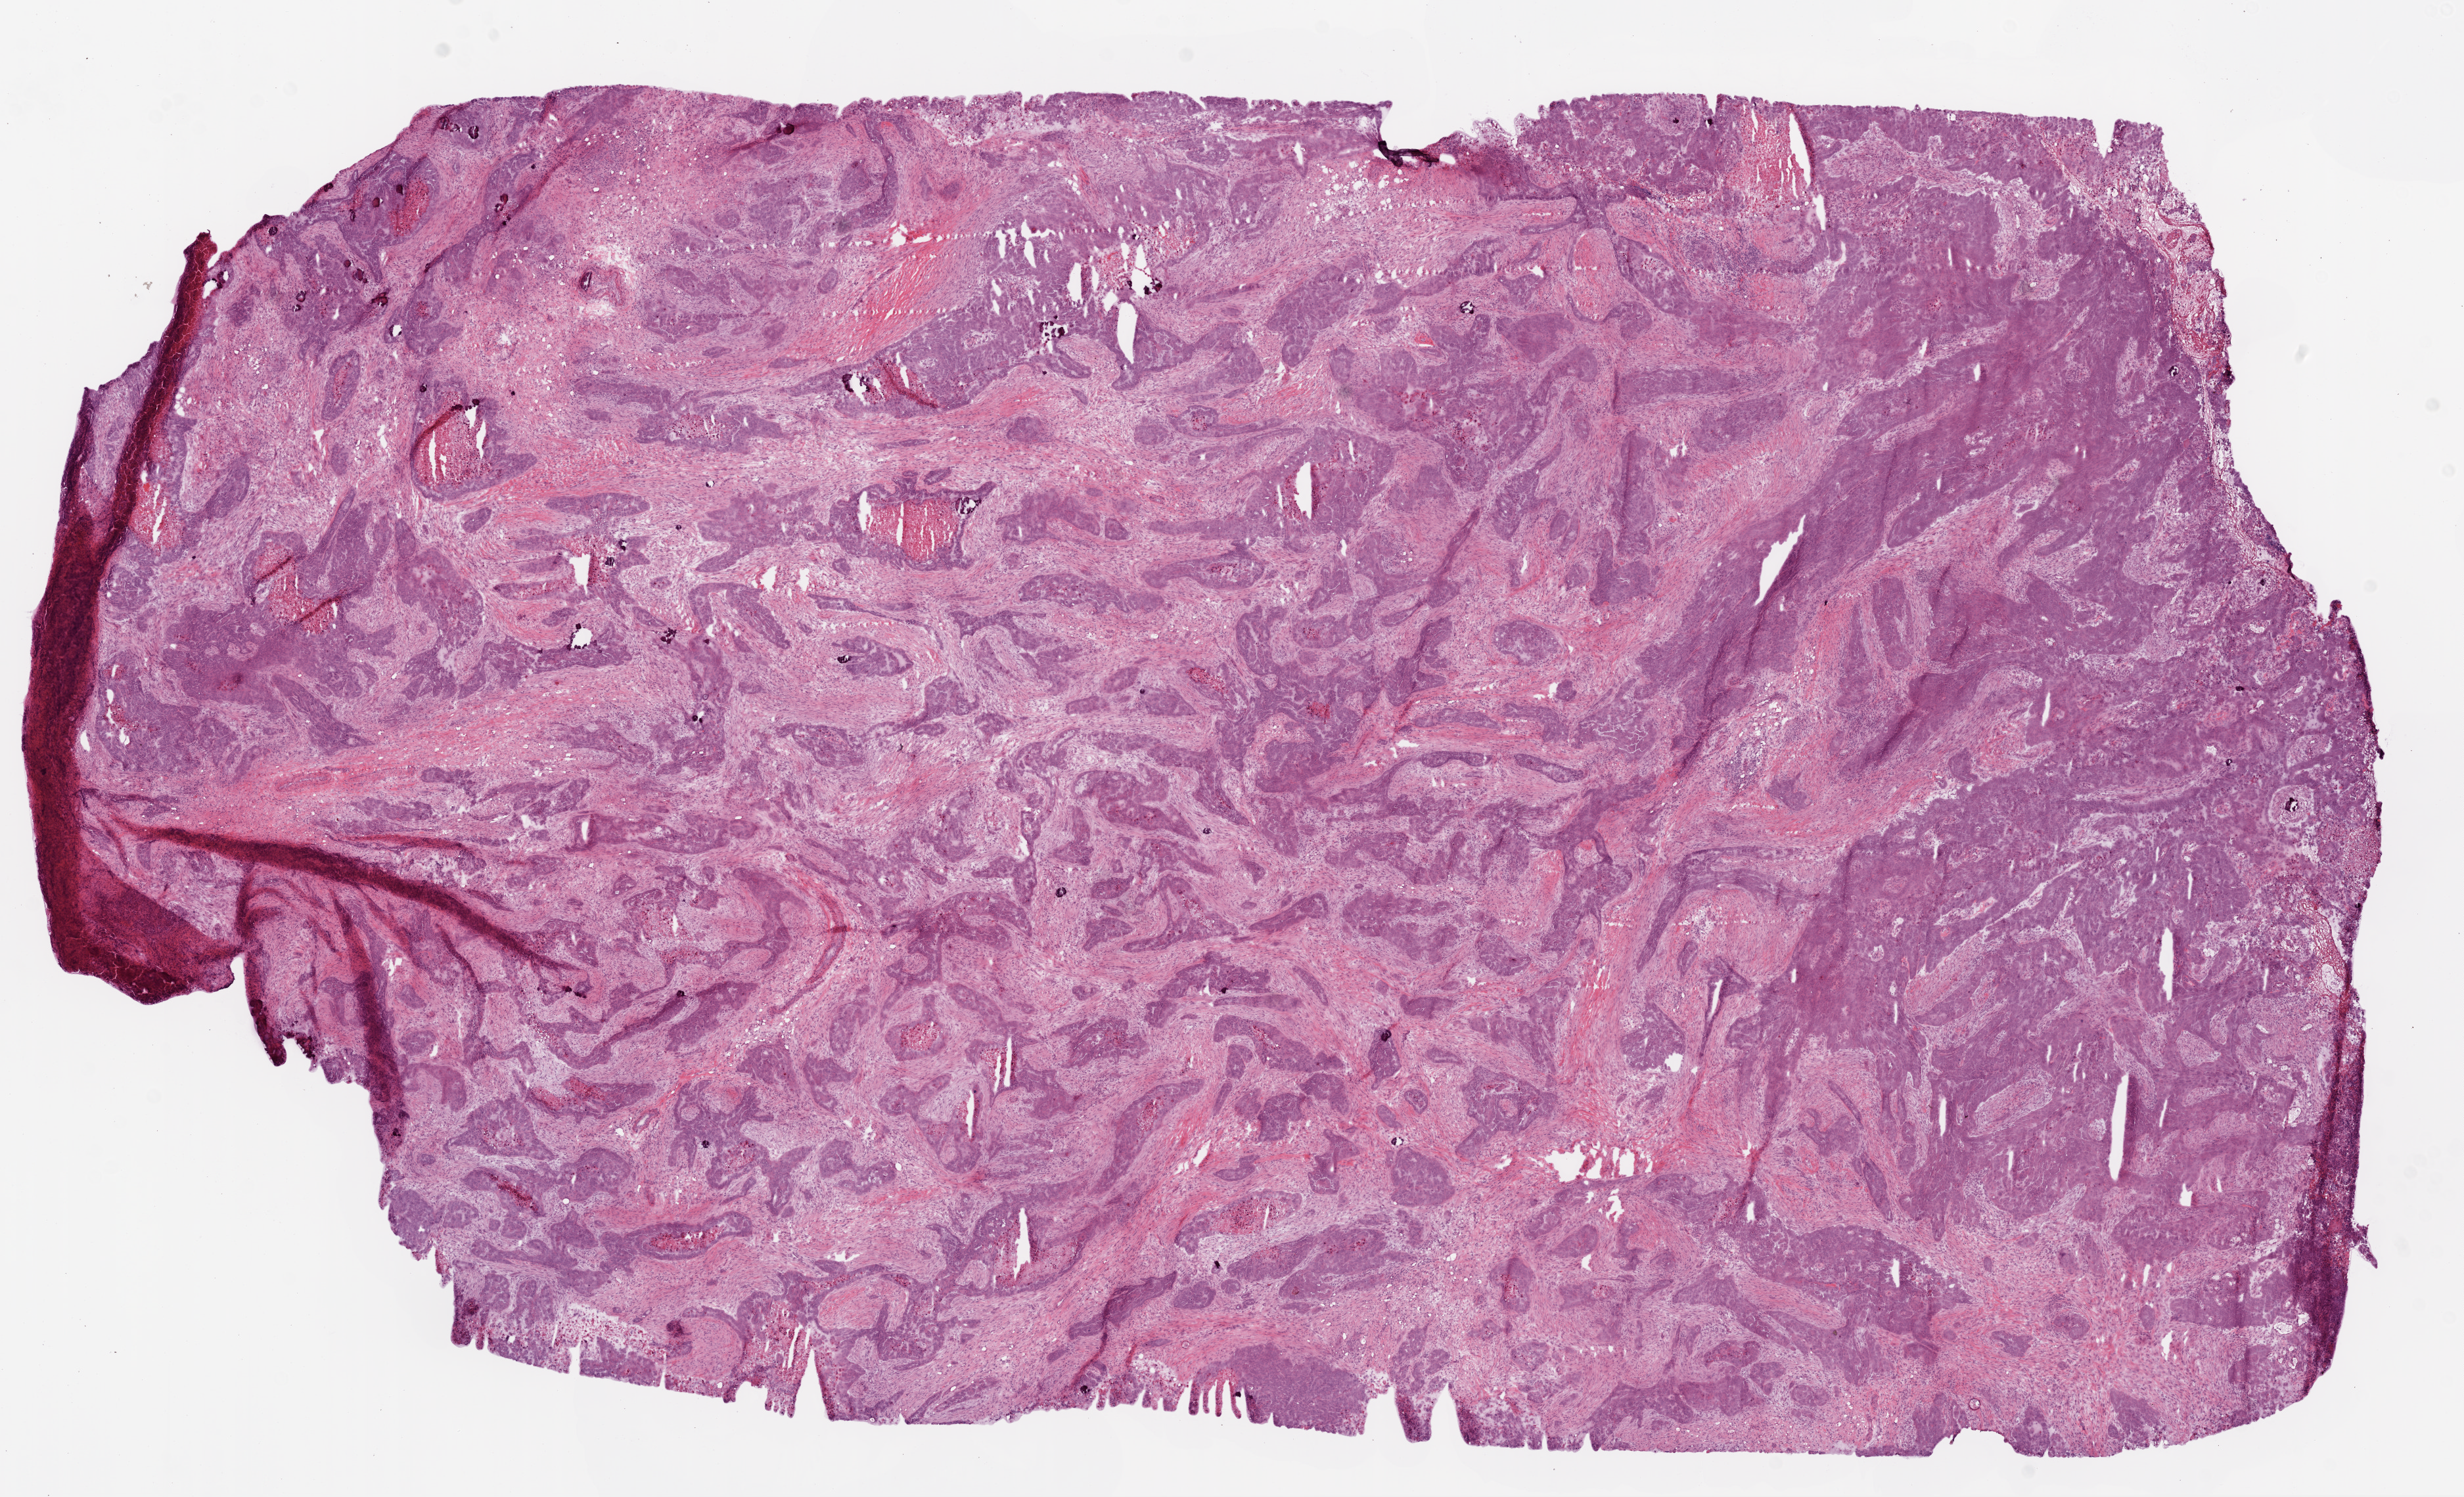
H&E whole-slide image — whole scanned area (about 15.0 x 9.1 mm) shown as a low-resolution overview, frozen section from the top of the tissue portion, ovary, primary tumour sample. Female patient; age at initial diagnosis 82 years. Histologic grade: G3 (poorly differentiated). Slide review estimates, as recorded: tumour cells 55%, tumour nuclei 70%, normal cells 0%, stromal cells 40%, necrosis 5%.
FIGO stage: IIIC. Diagnosis: Serous cystadenocarcinoma, NOS.